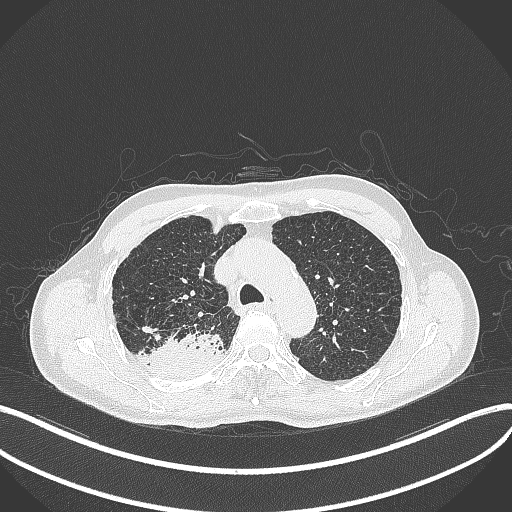
Chest CT, one axial slice. Lung window (W 1500 / L -600 HU). 1 mm slice thickness. 512 × 512 image matrix, field of view 400 × 400 mm. Male patient, age 79 years. Case-level facts recorded for this patient, not image findings: clinical TNM (as recorded): T3 N0 M0.
Outlined on this slice (rectangle marked by the reading radiologist):
- lung tumour (recorded histology: adenocarcinoma): bounding box (x1, y1, x2, y2) in pixels: (143, 325, 225, 379)